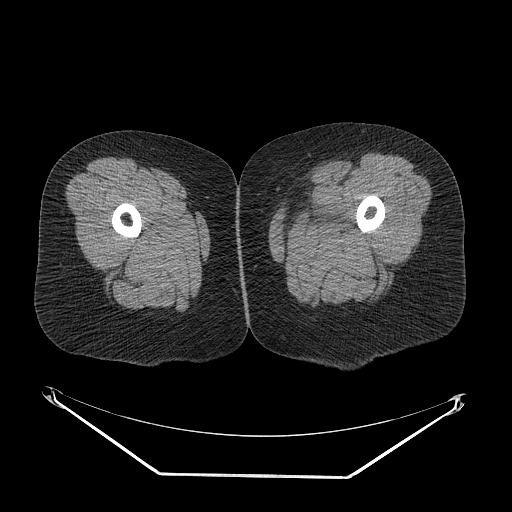
CT of an extremity soft-tissue mass (from a PET/CT study), one axial slice; position 11 of 267 along the scan axis; 140 kVp; soft-tissue window (W 400 / L 40 HU); 3.75 mm slice thickness; 512 × 512 image matrix. Female patient. From the clinical record (not read from this slice): histological type: myxofibrosarcoma; grade: intermediate; site of the primary tumour: left thigh.
Structures marked on this image (expert contour drawn on MRI and transferred to this co-registered scan by the dataset authors):
- gross tumour volume including surrounding oedema: bounding box (x1, y1, x2, y2) in pixels: (279, 199, 352, 241)